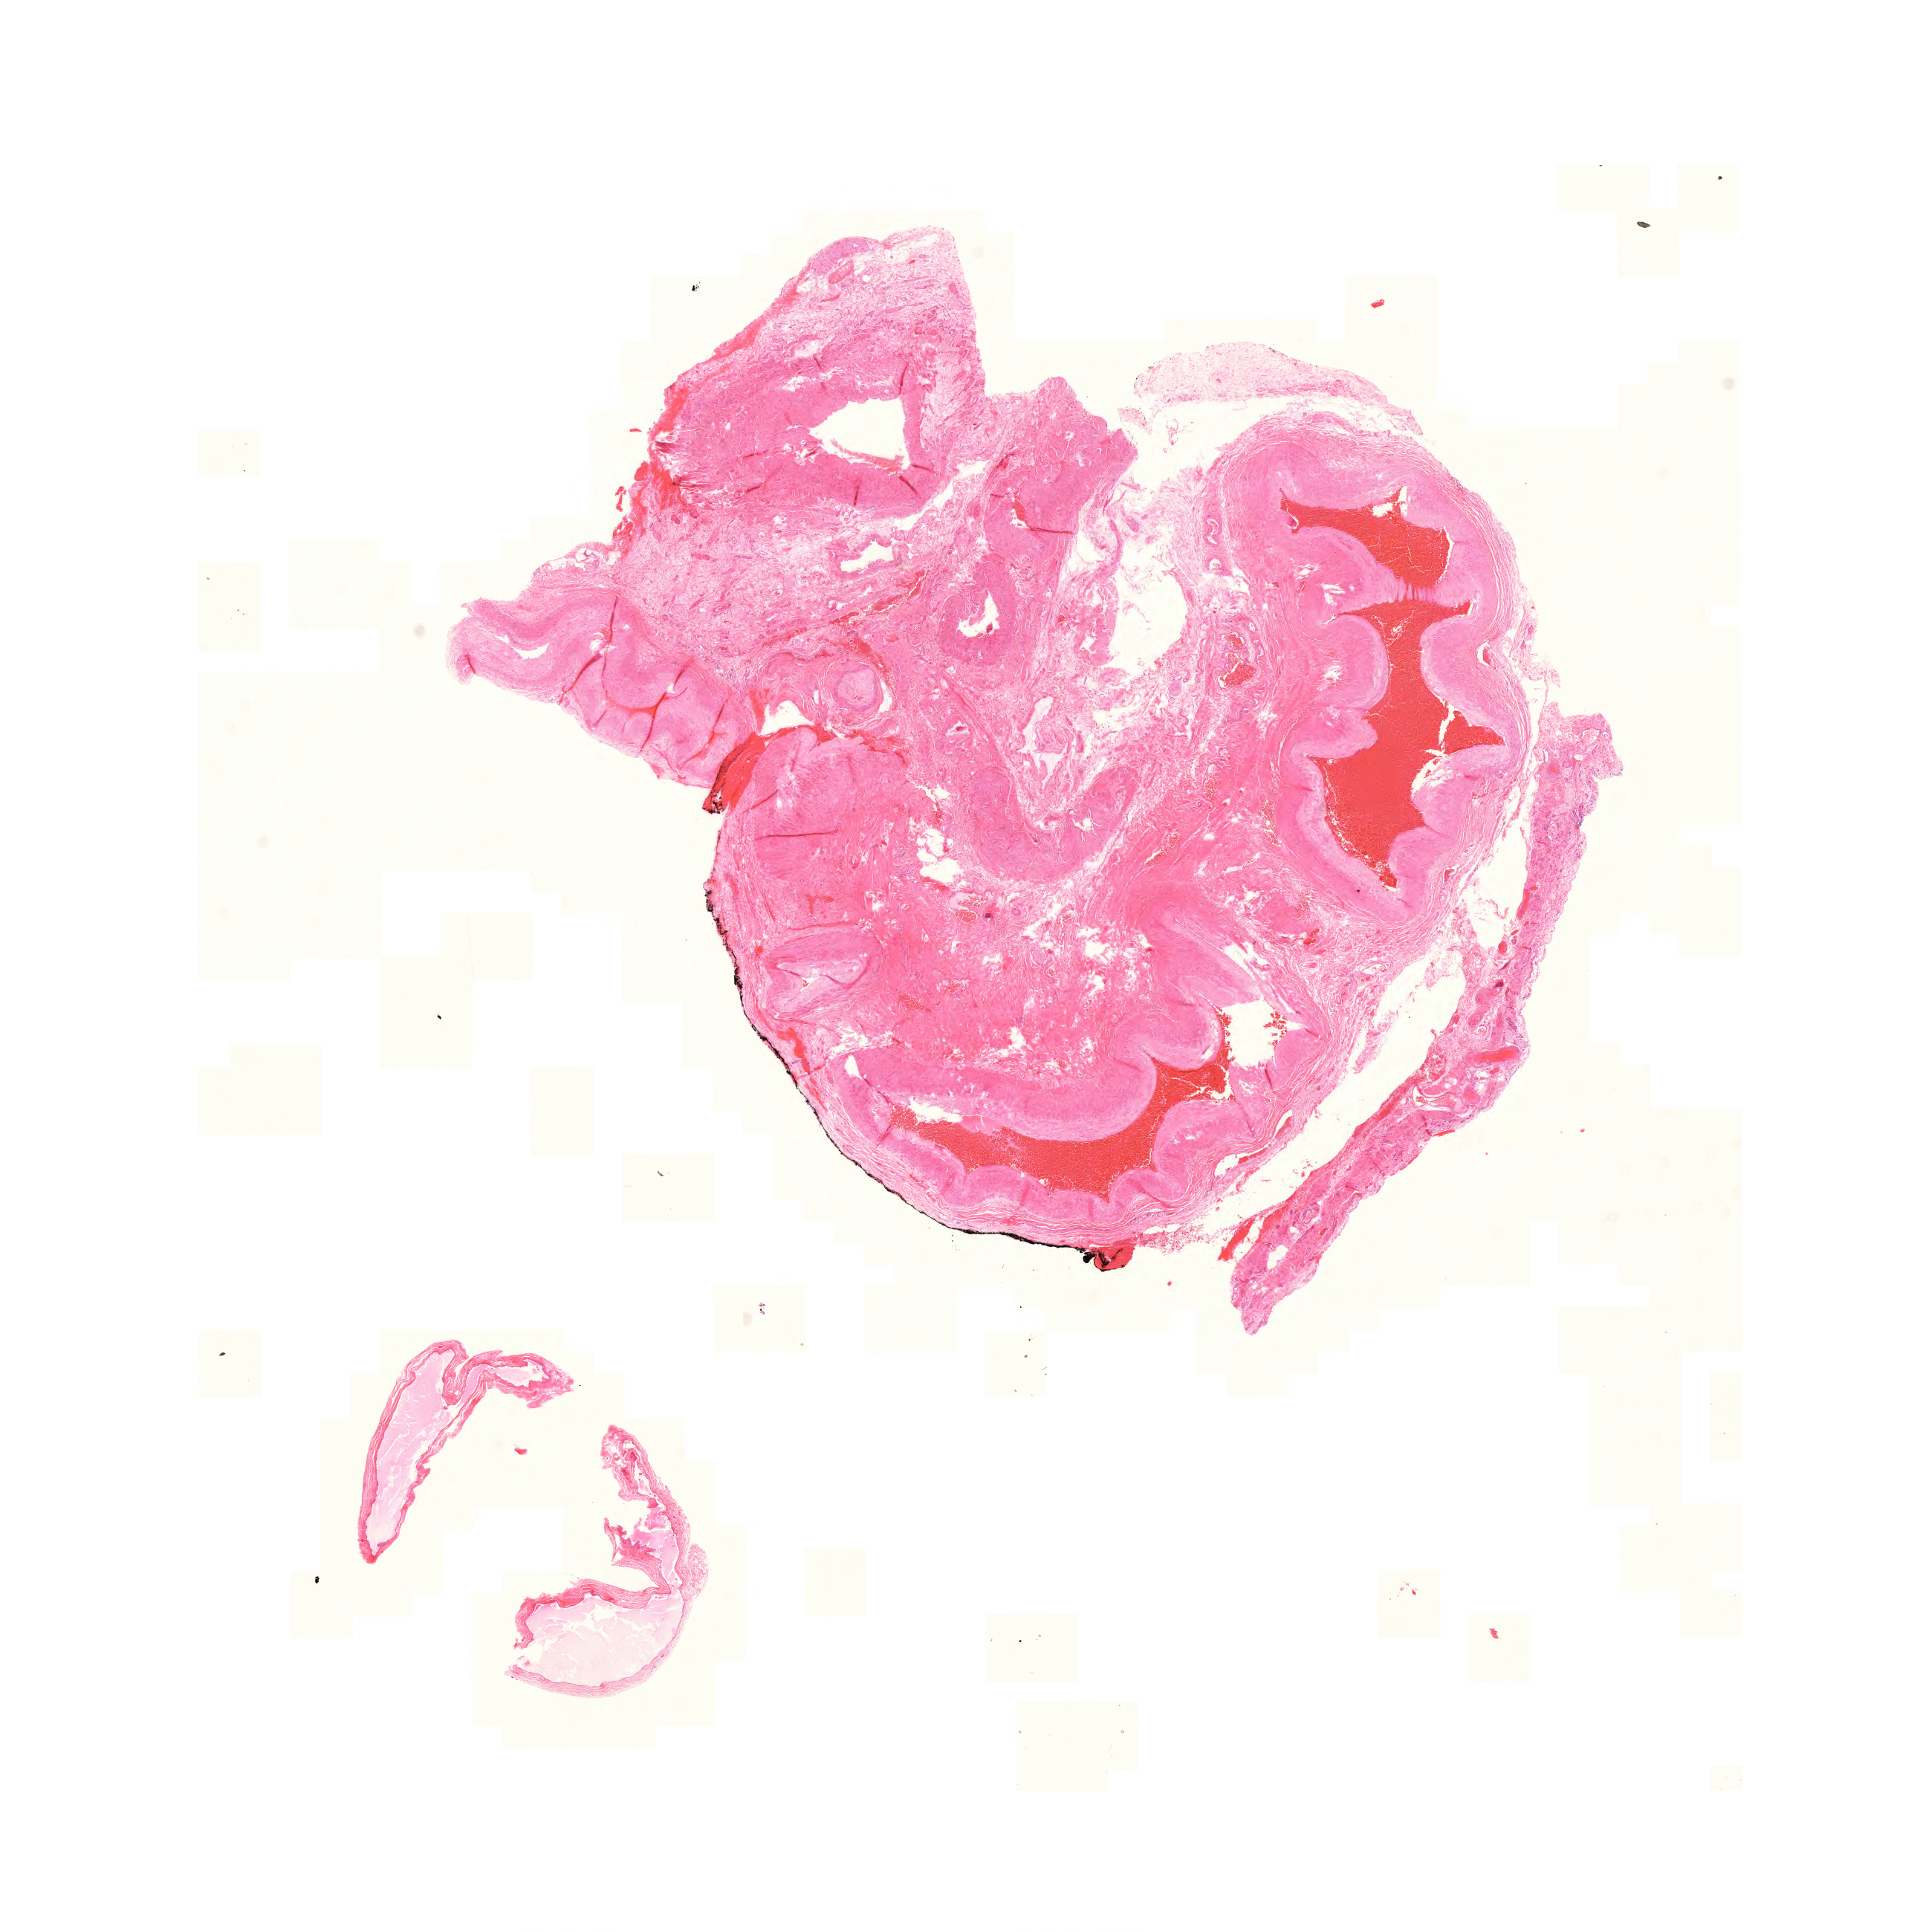
Whole-slide histology image, Hematoxylin and eosin (H&E) stained — a low-resolution overview of the entire scanned area, about 19.2 x 19.3 mm (acquisition: 20x scan); formalin-fixed paraffin-embedded (FFPE) diagnostic section; colon, primary tumour sample. Male patient; age at initial diagnosis 82 years.
Histologic diagnosis: Adenocarcinoma, NOS. AJCC pathologic stage: IIA (7th edition).